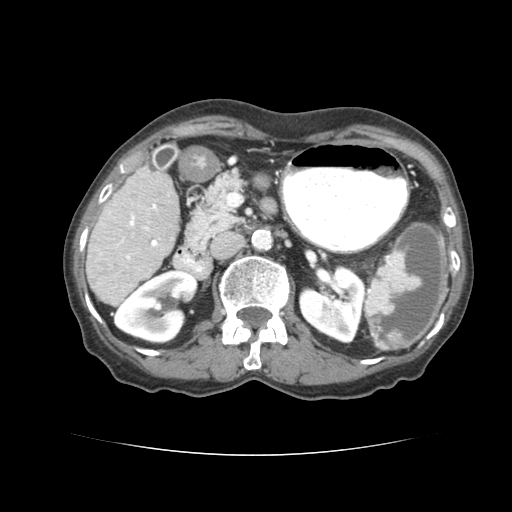
Contrast-enhanced abdominal CT (liver protocol), one axial slice; position 29 of 77 along the scan axis; 120 kVp; soft-tissue window (W 400 / L 40 HU); 512 × 512 image matrix, field of view 340 × 340 mm. Case-level facts recorded for this patient, not image findings: diagnosis: hepatocellular carcinoma (patient treated with transarterial chemoembolisation; whether this scan precedes or follows treatment is not stated here); TNM stage (as recorded): Stage-I; Child-Pugh class: A; tumour nodularity: uninodular.
Annotated regions visible in this slice (semi-automatic segmentation, software-assisted and operator-edited):
- liver parenchyma outside the tumour (the mass and vessels are separate outlines, so this box may not span the whole liver): box from (x=85, y=164) to (x=178, y=301) px
- liver vessels: (x=121, y=200)–(x=156, y=243)